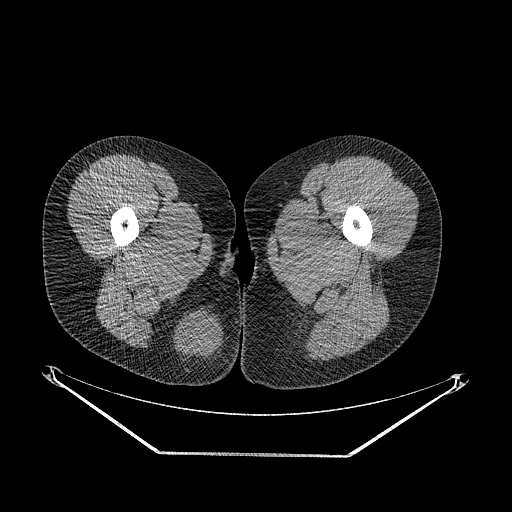
CT of an extremity soft-tissue mass (from a PET/CT study), one axial slice; position 21 of 267 along the scan axis; reconstruction kernel STANDARD; soft-tissue window (W 400 / L 40 HU); 512 × 512 image matrix. Female patient. From the clinical record (not read from this slice): histological type: epithelioid sarcoma; grade: intermediate; site of the primary tumour: right buttock.
Structures marked on this image (expert contour drawn on MRI and transferred to this co-registered scan by the dataset authors):
- gross tumour volume including surrounding oedema: bounding box <171,308,231,380> (left, top, right, bottom; pixels)
- gross tumour volume (mass): <176,313,222,357>